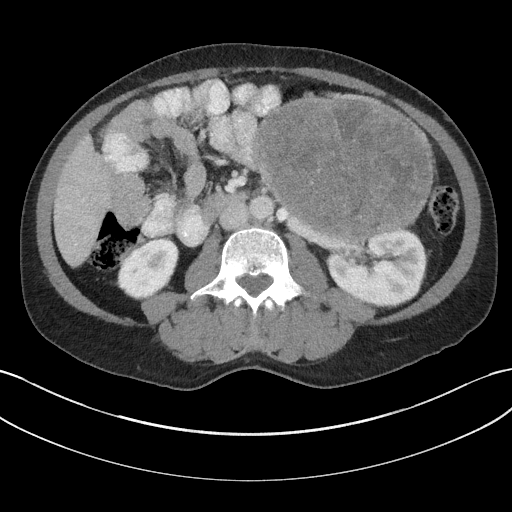
Contrast-enhanced abdominal CT, one axial slice. Slice 84 of 147 in the series (ordered by position). Intravenous contrast given. Soft-tissue window (W 400 / L 40 HU). 3 mm slice thickness. 512 × 512 image matrix, field of view 384 × 384 mm. Male patient, age 58 years. Case-level facts recorded for this patient, not image findings: diagnosis: adrenocortical carcinoma; tumour side: left adrenal; tumour size at pathology: 22 cm.
Structures marked on this image (semi-automatic segmentation, software-assisted and operator-edited):
- mass: box from (x=257, y=99) to (x=433, y=236) px